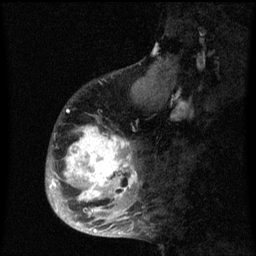
Breast MRI (dynamic contrast-enhanced), one sagittal slice. Position 22 of 60 along the scan axis. Dynamic contrast-enhanced series, image 2 of 3 at this slice position (ordered by acquisition). 1.5 T. TE 4.2 ms, TR 8 ms. 2 mm slice thickness. 256 × 256 image matrix. Patient: female, 50 years.
Outlined on this slice (semi-automatic segmentation, software-assisted and operator-edited):
- analysis volume of interest (the breast-tissue region the enhancement analysis was run in; not a lesion): bounding box (x1, y1, x2, y2) in pixels: (46, 90, 142, 216)
- tumour enhancement mask (voxels above the 70 % enhancement threshold inside the analysis volume of interest): (49, 126, 137, 216)